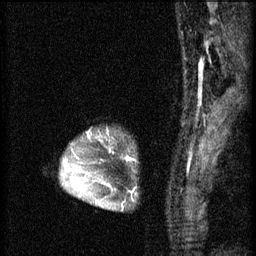
Breast MRI (dynamic contrast-enhanced), one sagittal slice; slice 48 of 60 in the series (ordered by position); 3 images stored at this slice position (order not interpretable as contrast timing); 1.5 T; TE 4.2 ms, TR 8.2 ms; 2 mm slice thickness; 256 × 256 image matrix, field of view 180 × 180 mm. Female patient, age 45 years.
Structures marked on this image (semi-automatically segmented with operator editing):
- analysis volume of interest (the breast-tissue region the enhancement analysis was run in; not a lesion): bounding box (x1, y1, x2, y2) in pixels: (62, 130, 135, 211)
- tumour enhancement mask (voxels above the 70 % enhancement threshold inside the analysis volume of interest): (74, 132, 123, 209)